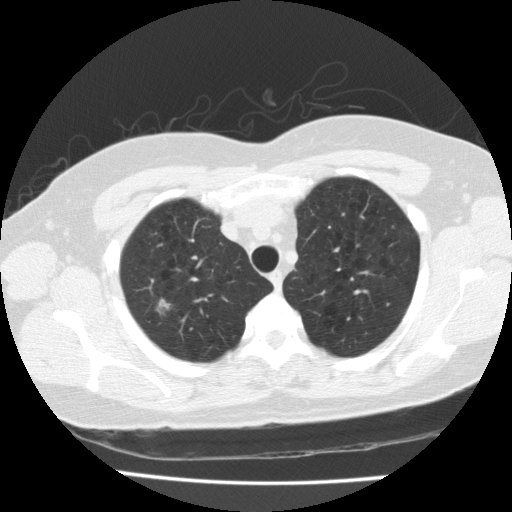
Low-dose screening chest CT, one axial slice; slice 145 of 175 in the series (ordered by position); reconstruction kernel FC10; 120 kVp; lung window (W 1500 / L -600 HU); 2 mm slice thickness; 512 × 512 image matrix.
Annotated regions visible in this slice (manually delineated by an expert):
- lesion 1 (tumor, upper lobe of right lung): bounding box (x1, y1, x2, y2) in pixels: (157, 299, 170, 312)